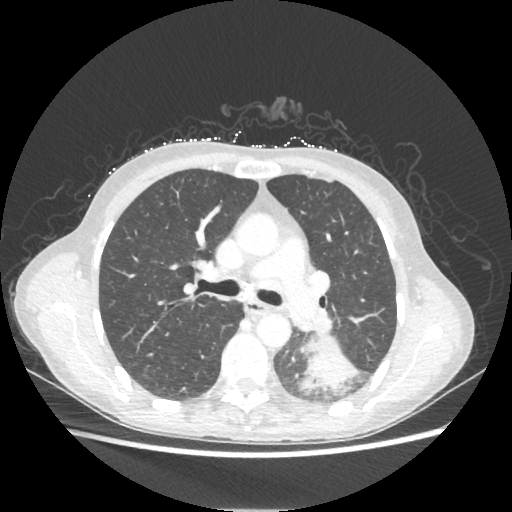
Chest CT, one axial slice. Position 136 of 221 along the scan axis. 80 kVp. Lung window (W 1500 / L -600 HU). 1.25 mm slice thickness. 512 × 512 image matrix. Female patient, age 53 years. From the clinical record (not read from this slice): clinical TNM (as recorded): T3 N0 M0.
Structures marked on this image (rectangle marked by the reading radiologist):
- lung tumour (recorded histology: adenocarcinoma): bounding box <304,336,359,390> (left, top, right, bottom; pixels)